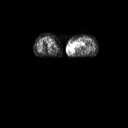
FDG PET of an extremity soft-tissue mass (from a PET/CT study), one axial slice; position 12 of 91 along the scan axis; 3.27 mm slice thickness; 128 × 128 image matrix. Patient: female, 74 years. Case-level facts recorded for this patient, not image findings: histological type: pleomorphic leiomyosarcoma; grade: high; site of the primary tumour: left thigh.
Outlined on this slice (expert contour drawn on MRI and transferred to this co-registered scan by the dataset authors):
- gross tumour volume including surrounding oedema: box from (x=71, y=38) to (x=87, y=52) px